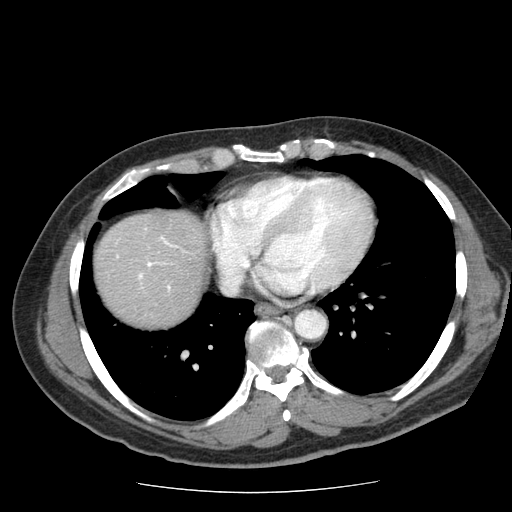
Contrast-enhanced abdominal CT (liver protocol), one axial slice. Soft-tissue window (W 400 / L 40 HU). 512 × 512 image matrix, field of view 360 × 360 mm. Case-level facts recorded for this patient, not image findings: diagnosis: hepatocellular carcinoma (patient treated with transarterial chemoembolisation; whether this scan precedes or follows treatment is not stated here); TNM stage (as recorded): Stage-IIIA; Child-Pugh class: A; tumour differentiation: well differentiated; tumour nodularity: multinodular.
Structures marked on this image (semi-automatic segmentation, software-assisted and operator-edited):
- liver parenchyma outside the tumour (the mass and vessels are separate outlines, so this box may not span the whole liver): box from (x=94, y=212) to (x=206, y=326) px
- liver vessels: (x=116, y=237)–(x=177, y=290)